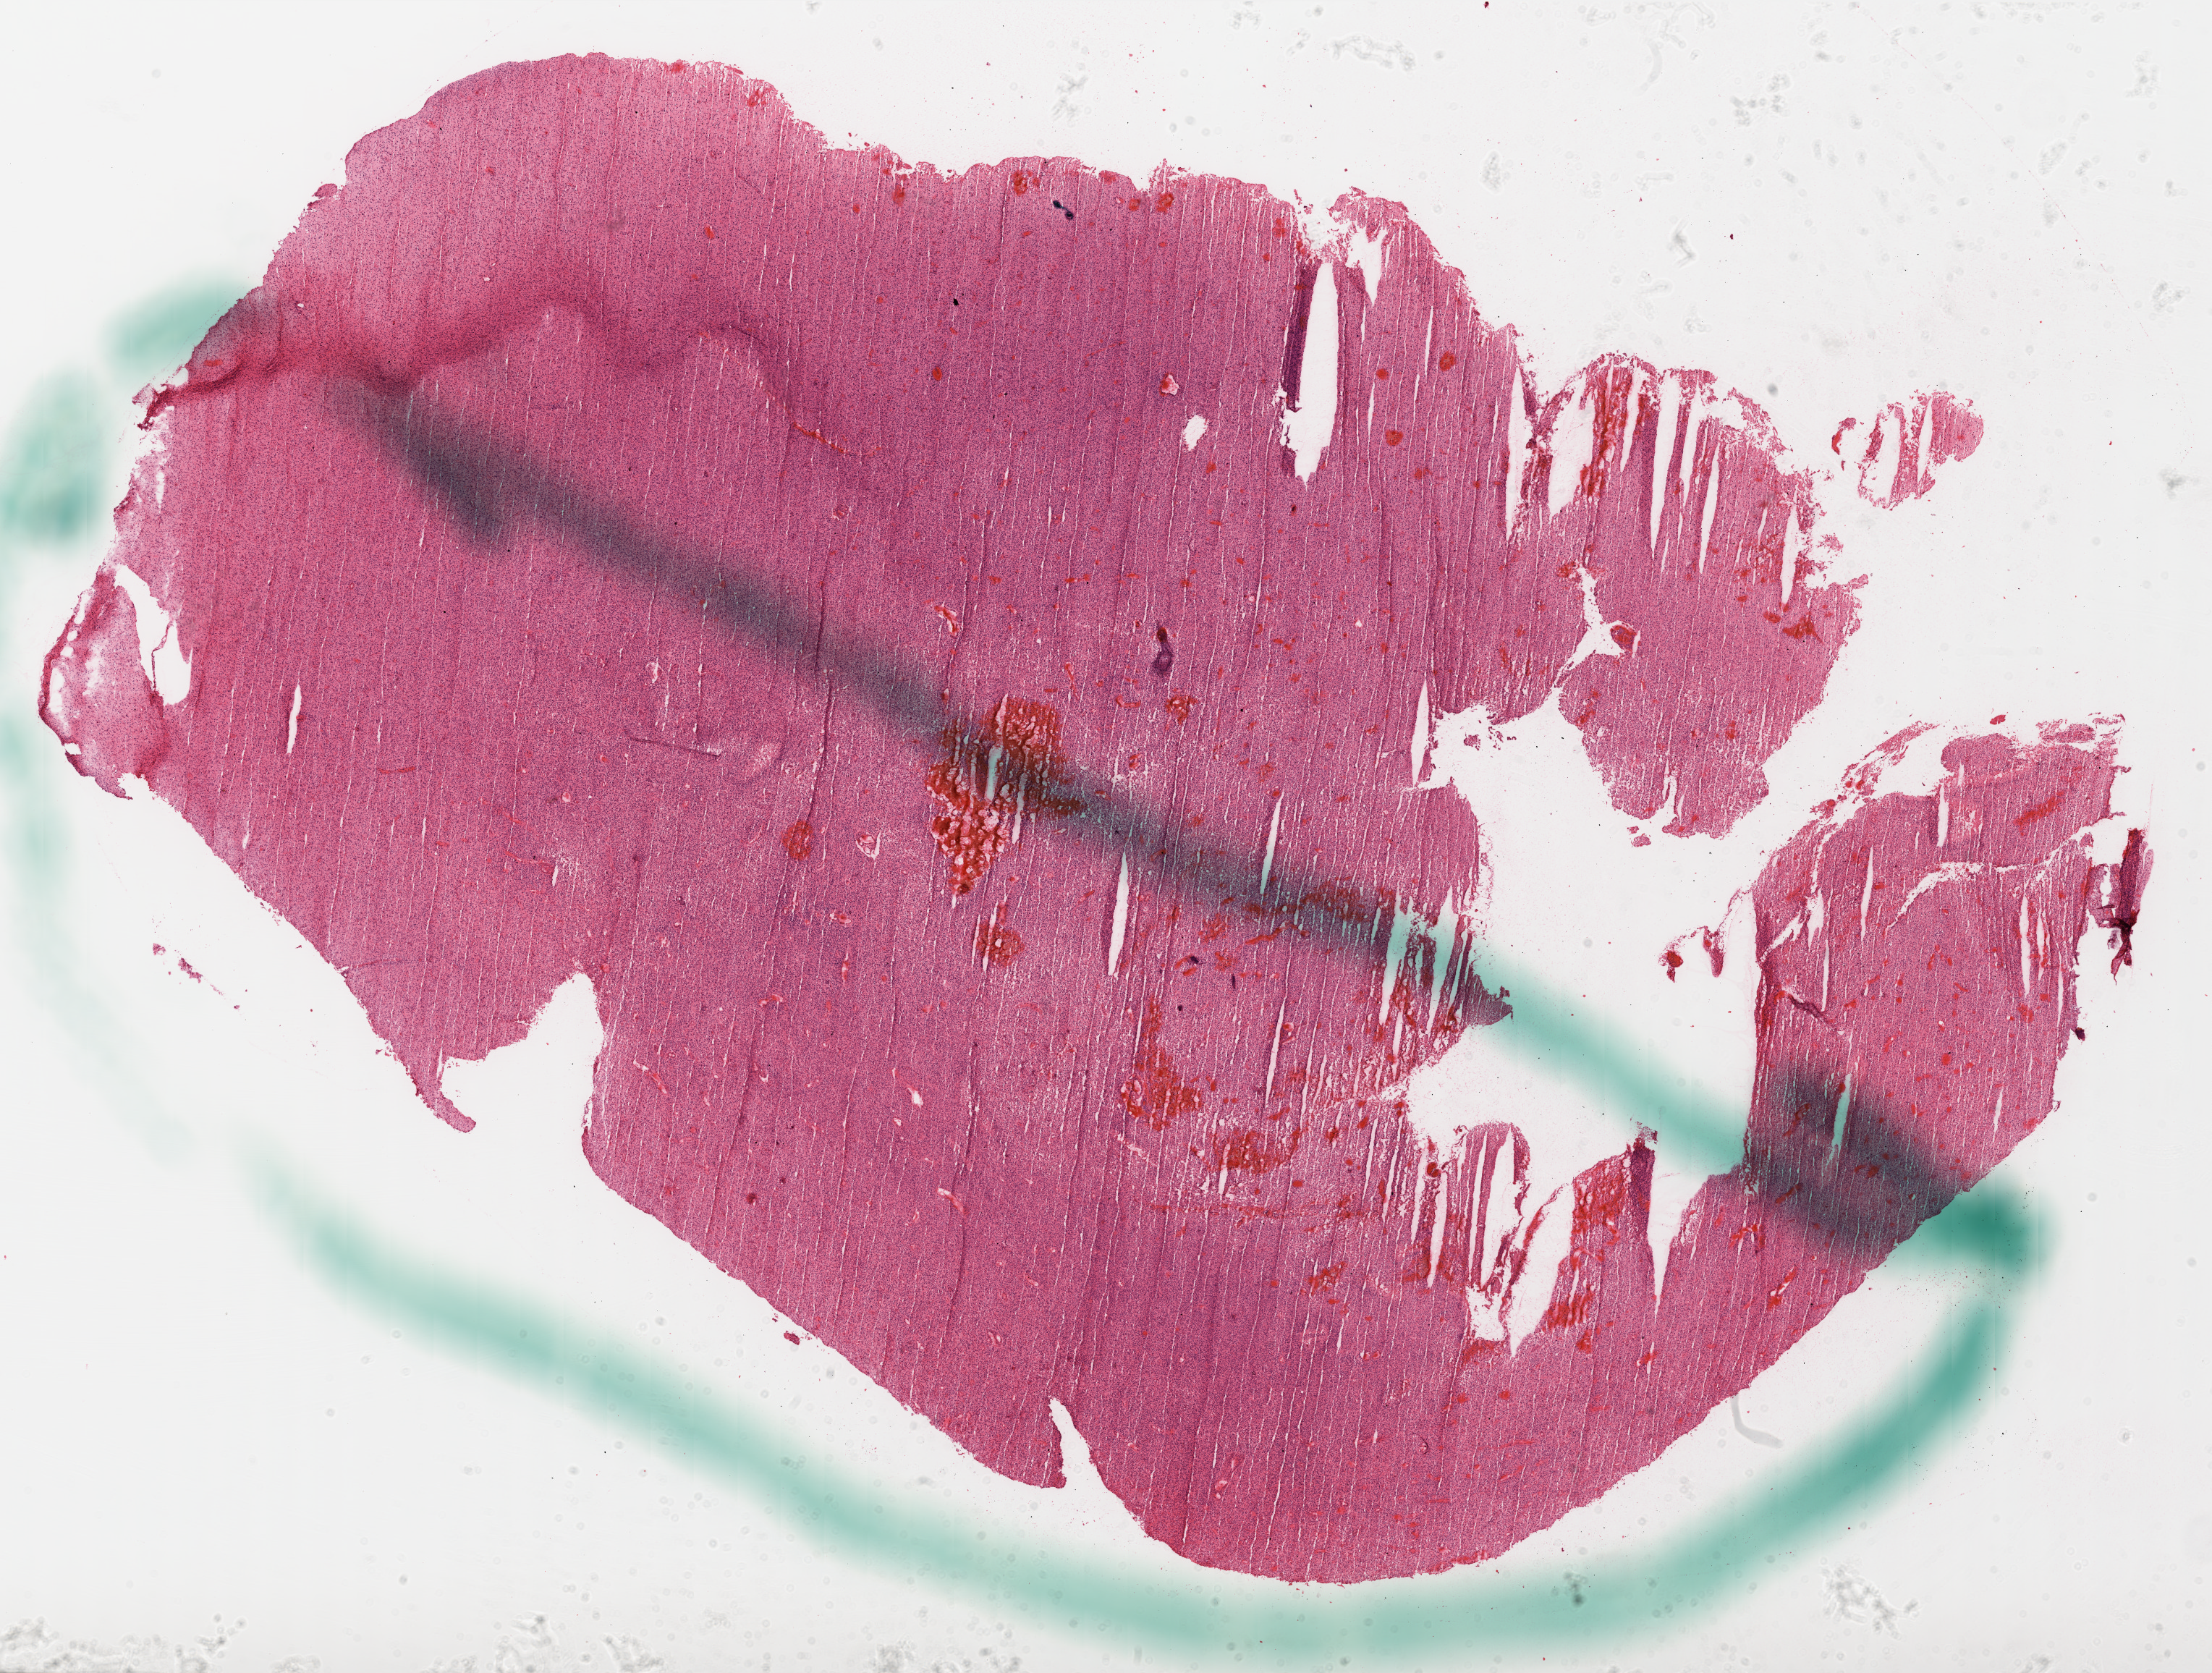
Whole-slide histology image, H&E, shown as a low-resolution overview of the whole scanned area (about 24.6 x 18.6 mm, slide scanned at 20x). Frozen section from the top of the tissue portion. Primary tumour sample from the brain. Male, age 50 years at initial diagnosis. Composition of this section per pathologist review: tumour cells 100%, tumour nuclei 100%, normal cells 0%, stromal cells 0%, necrosis 5%.
• diagnosis: Glioblastoma